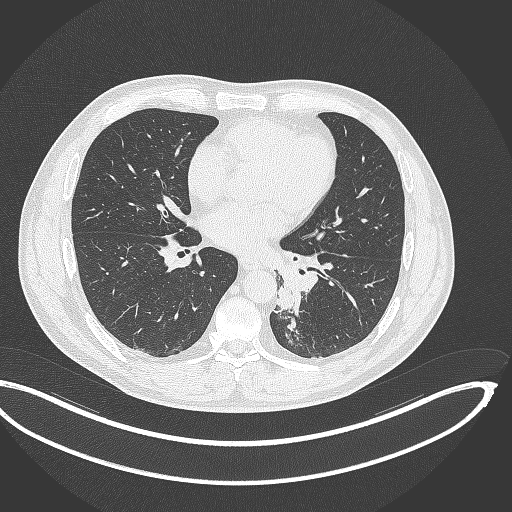
Chest CT, one axial slice. Slice 161 of 362 in the series (ordered by position). Reconstruction kernel B70f. Lung window (W 1500 / L -600 HU). 512 × 512 image matrix. Patient: male, 50 years. Case-level facts recorded for this patient, not image findings: clinical TNM (as recorded): T2a N3 M0.
Structures marked on this image (rectangle marked by the reading radiologist):
- lung tumour (recorded histology: squamous cell carcinoma): bounding box (x1, y1, x2, y2) in pixels: (274, 279, 303, 313)